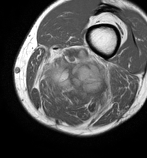
MRI of an extremity soft-tissue mass, one axial slice; MR volume resampled by the dataset authors to the PET/CT grid (not the native acquisition matrix); 3.27 mm slice thickness; 147 × 158 image matrix, field of view 144 × 154 mm. Male patient. Case-level facts recorded for this patient, not image findings: histological type: undifferentiated pleomorphic liposarcoma; grade: high; site of the primary tumour: left thigh.
Structures marked on this image (expert contour drawn on MRI and transferred to this co-registered scan by the dataset authors):
- gross tumour volume including surrounding oedema: bounding box [x1, y1, x2, y2] px = [32, 44, 115, 125]
- gross tumour volume (mass): [69, 65, 104, 100]